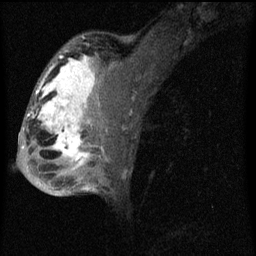
Breast MRI (dynamic contrast-enhanced), one sagittal slice. Slice 39 of 60 in the series (ordered by position). Dynamic contrast-enhanced series, image 2 of 4 at this slice position (ordered by acquisition). 1.5 T. TE 4.2 ms, TR 8 ms. 2 mm slice thickness. 256 × 256 image matrix, field of view 180 × 180 mm. Female patient, age 50 years.
Structures marked on this image (semi-automatically segmented with operator editing):
- analysis volume of interest (the breast-tissue region the enhancement analysis was run in; not a lesion): bounding box (x1, y1, x2, y2) in pixels: (26, 44, 124, 177)
- tumour enhancement mask (voxels above the 70 % enhancement threshold inside the analysis volume of interest): (28, 50, 109, 169)